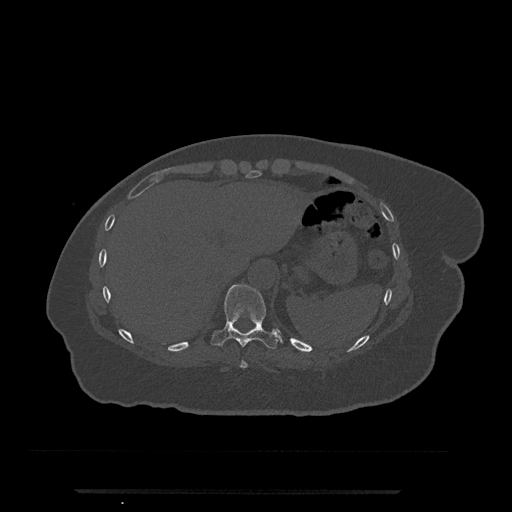
CT including the spine, one axial slice. Slice 289 of 797 in the series (ordered by position). Bone window (W 1800 / L 400 HU). 512 × 512 image matrix, field of view 440 × 440 mm. Patient: female, 51 years. Case-level facts recorded for this patient, not image findings: primary cancer: neuro.
Structures marked on this image (semi-automatically segmented with operator editing):
- T10 vertebra: bounding box [x1, y1, x2, y2] px = [211, 284, 280, 349]
- T9 vertebra: [239, 360, 248, 369]